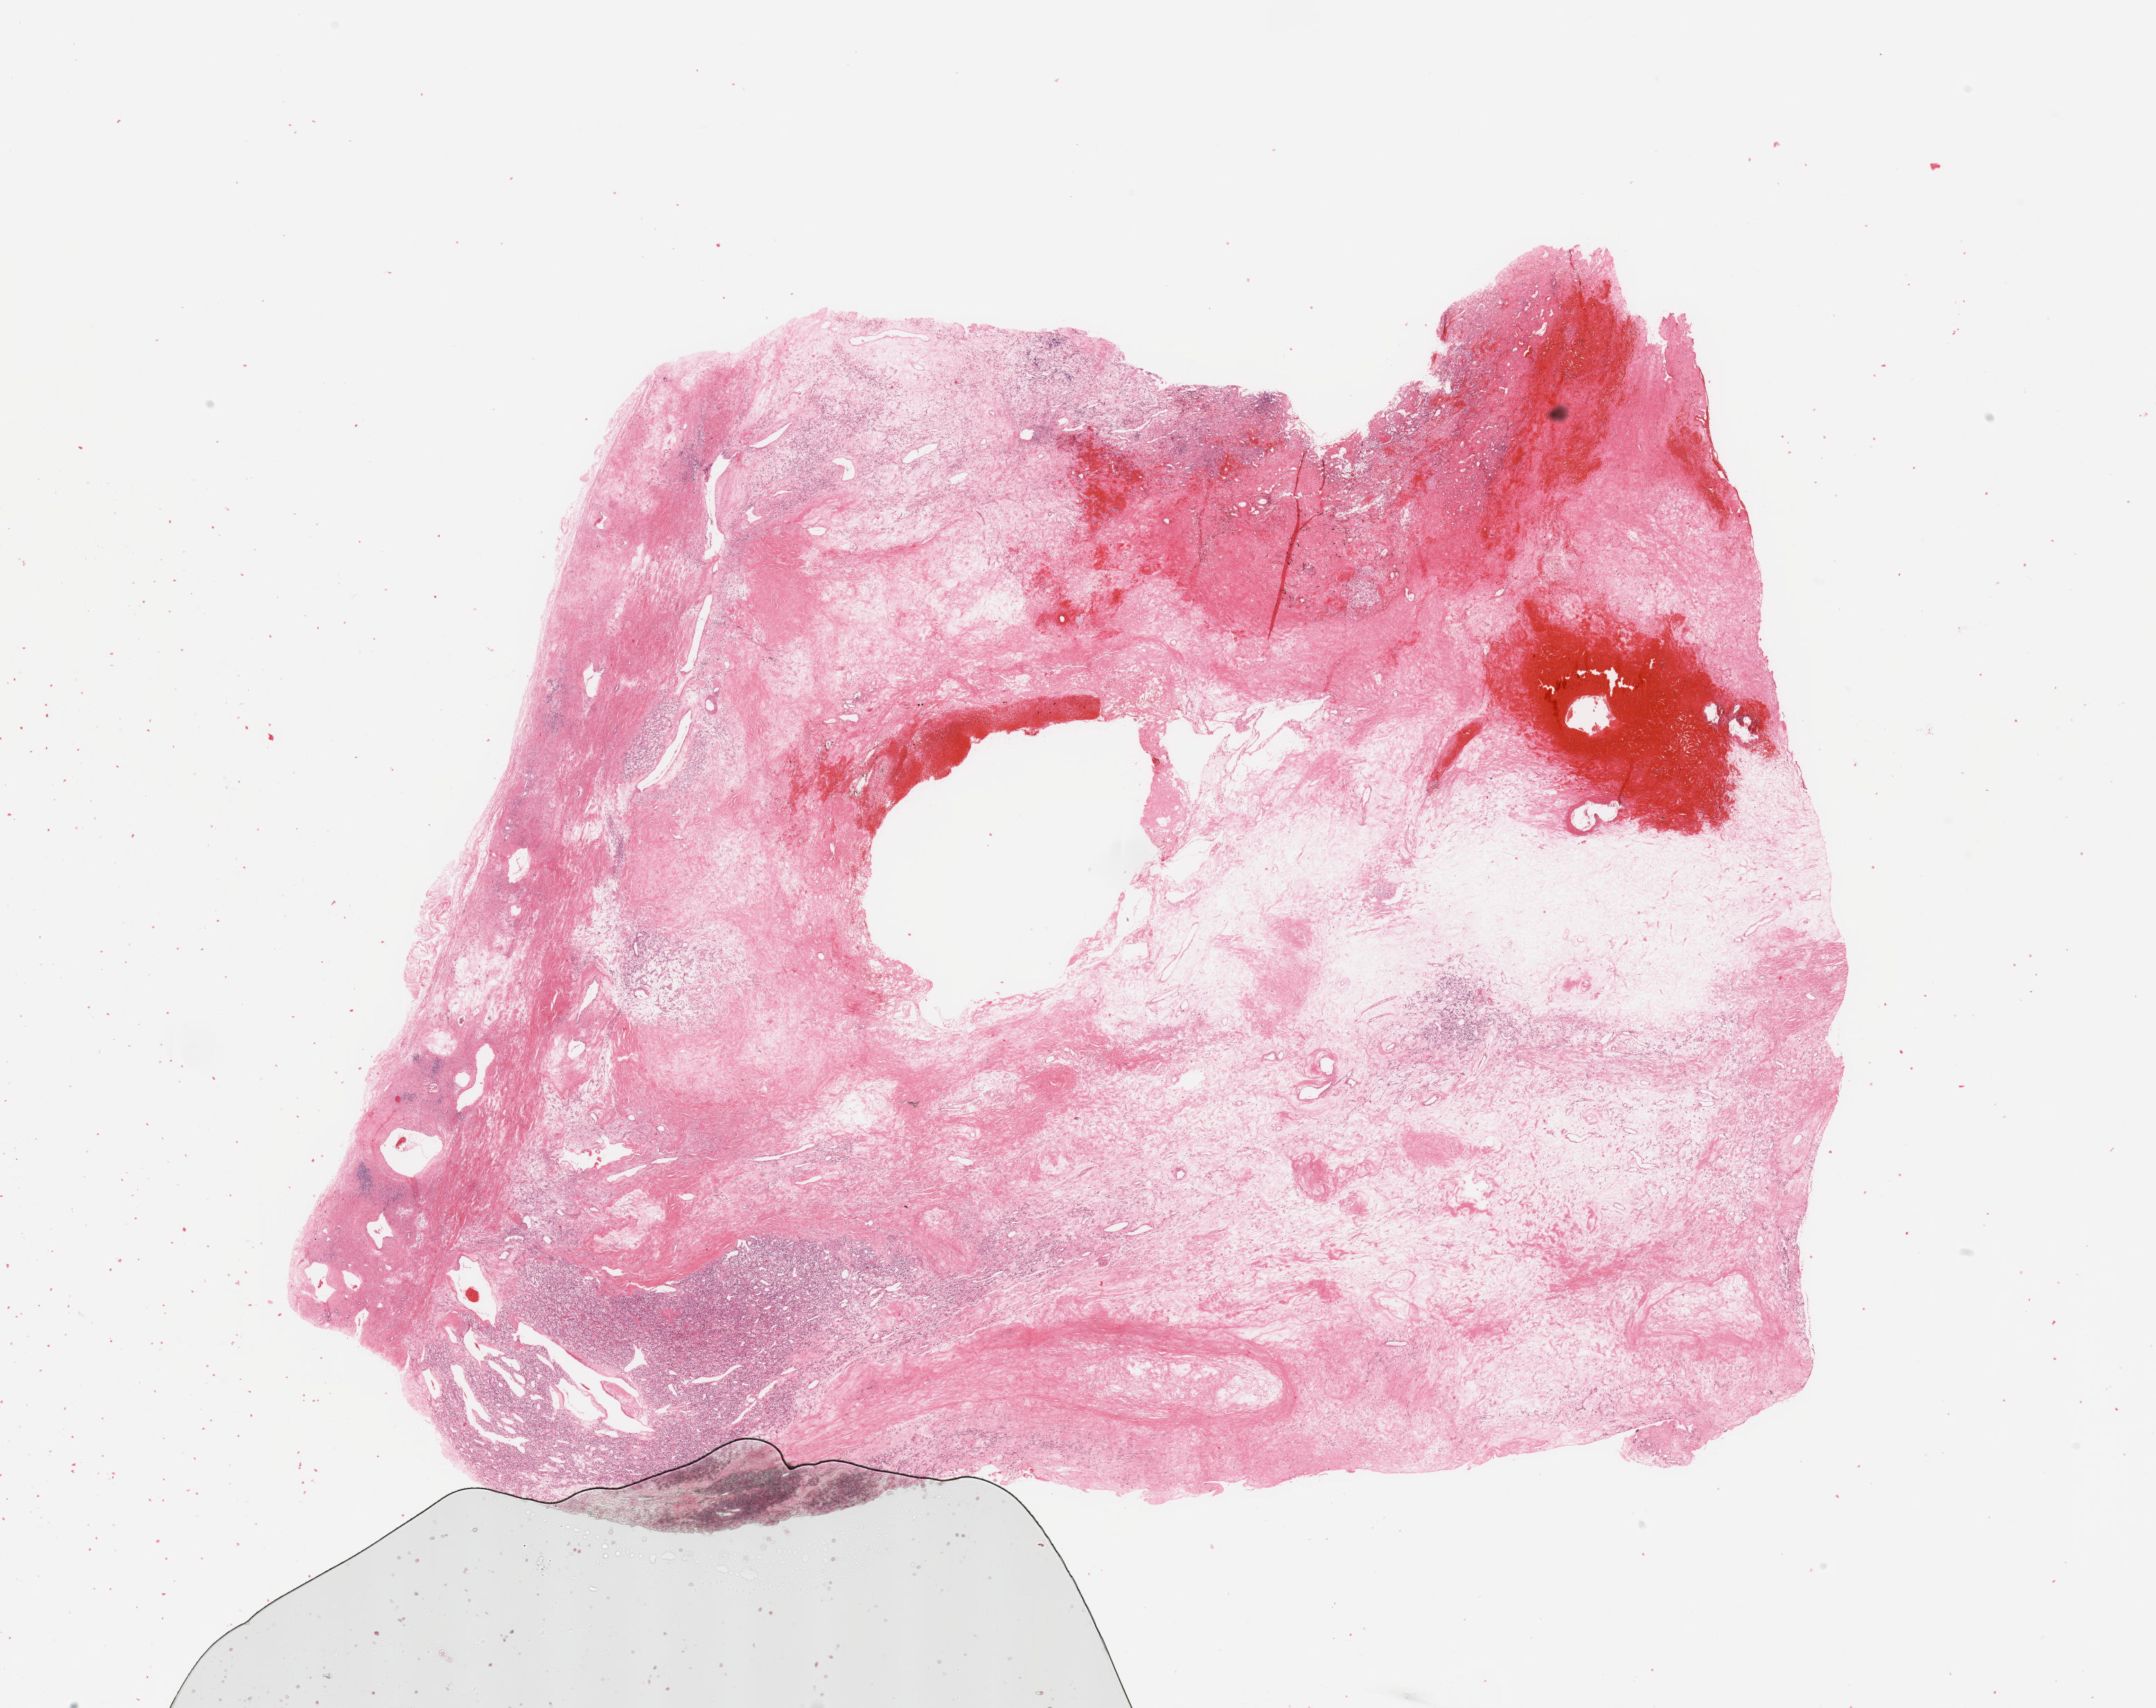
Hematoxylin and eosin (H&E) stained whole-slide image, low-resolution overview of the scanned area, about 24.6 x 19.5 mm. Tumour tissue sample, sampled site: kidney. Female, 57 y/o. Histologic grade: G2 (moderately differentiated). Pathologist review of this section (percent, as recorded): tumour nuclei 50%, necrosis 20%.
- diagnosis: Renal cell carcinoma, NOS
- AJCC pathologic stage: I